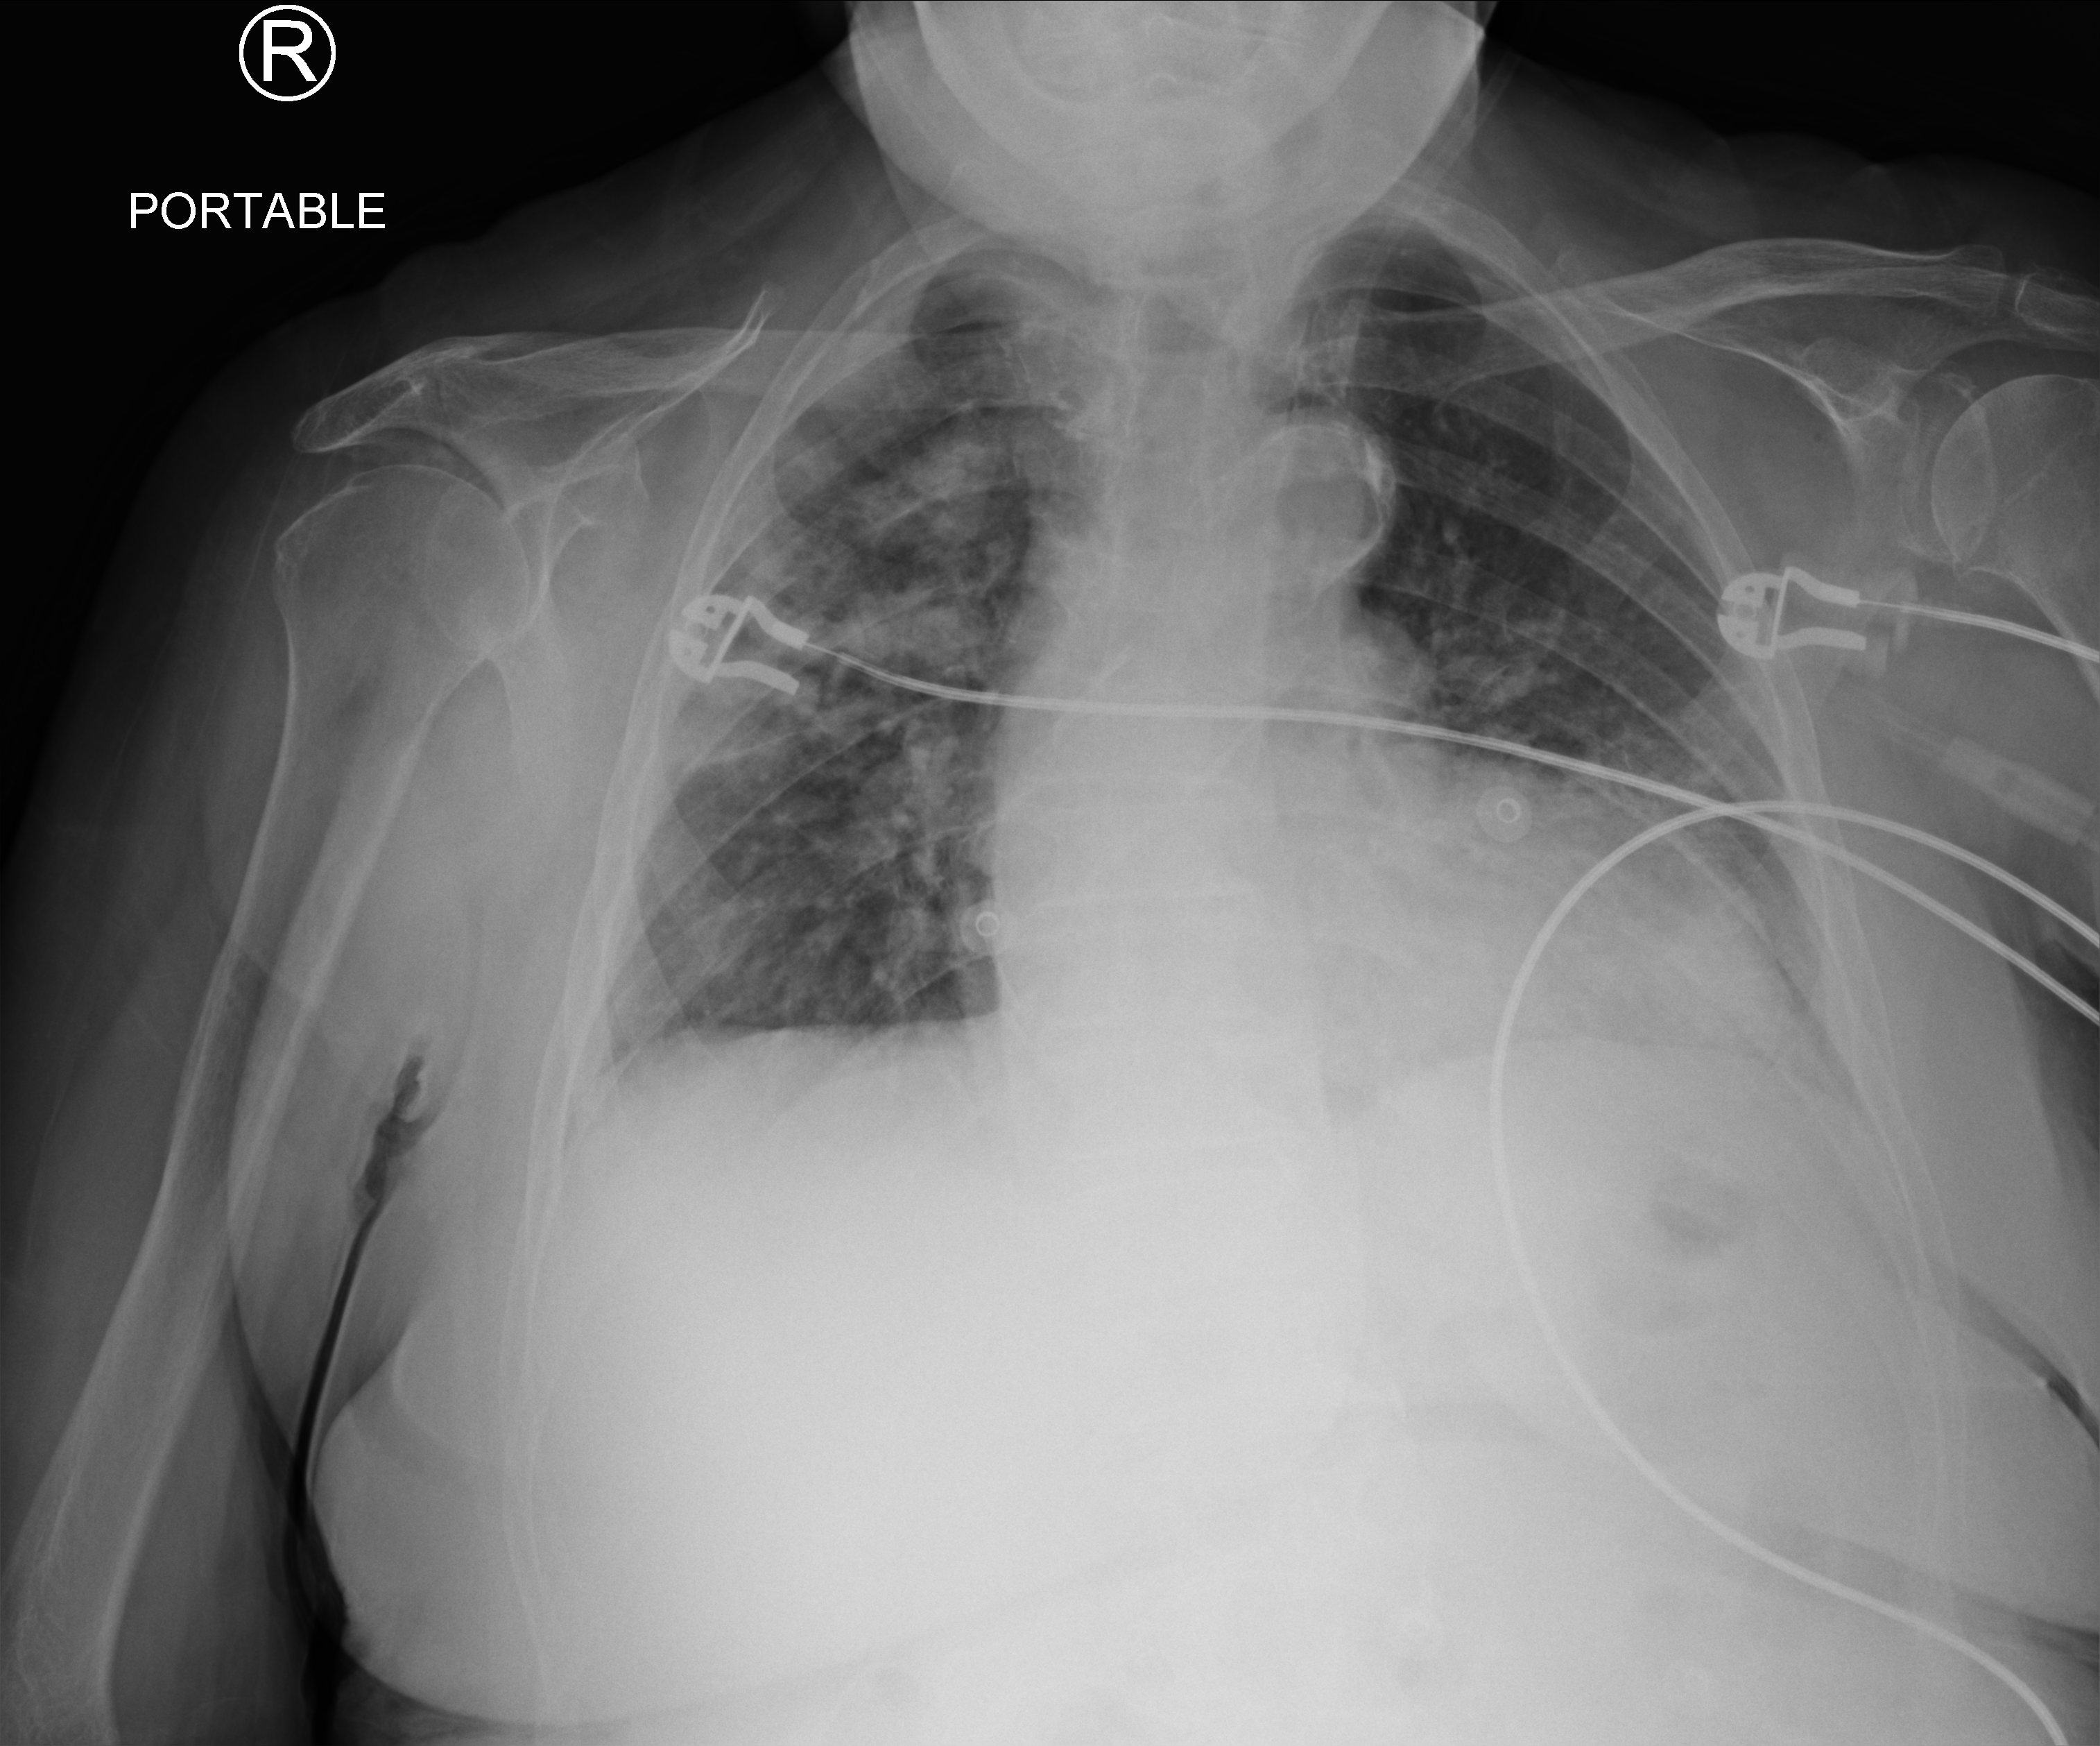
Portable chest radiograph; anteroposterior (AP) projection. Patient hospitalised with COVID-19; female, aged 75–90 years.
From the hospital-stay record, not from the radiograph (when in the stay this image was taken is not recorded): hypertension (admission record): yes.